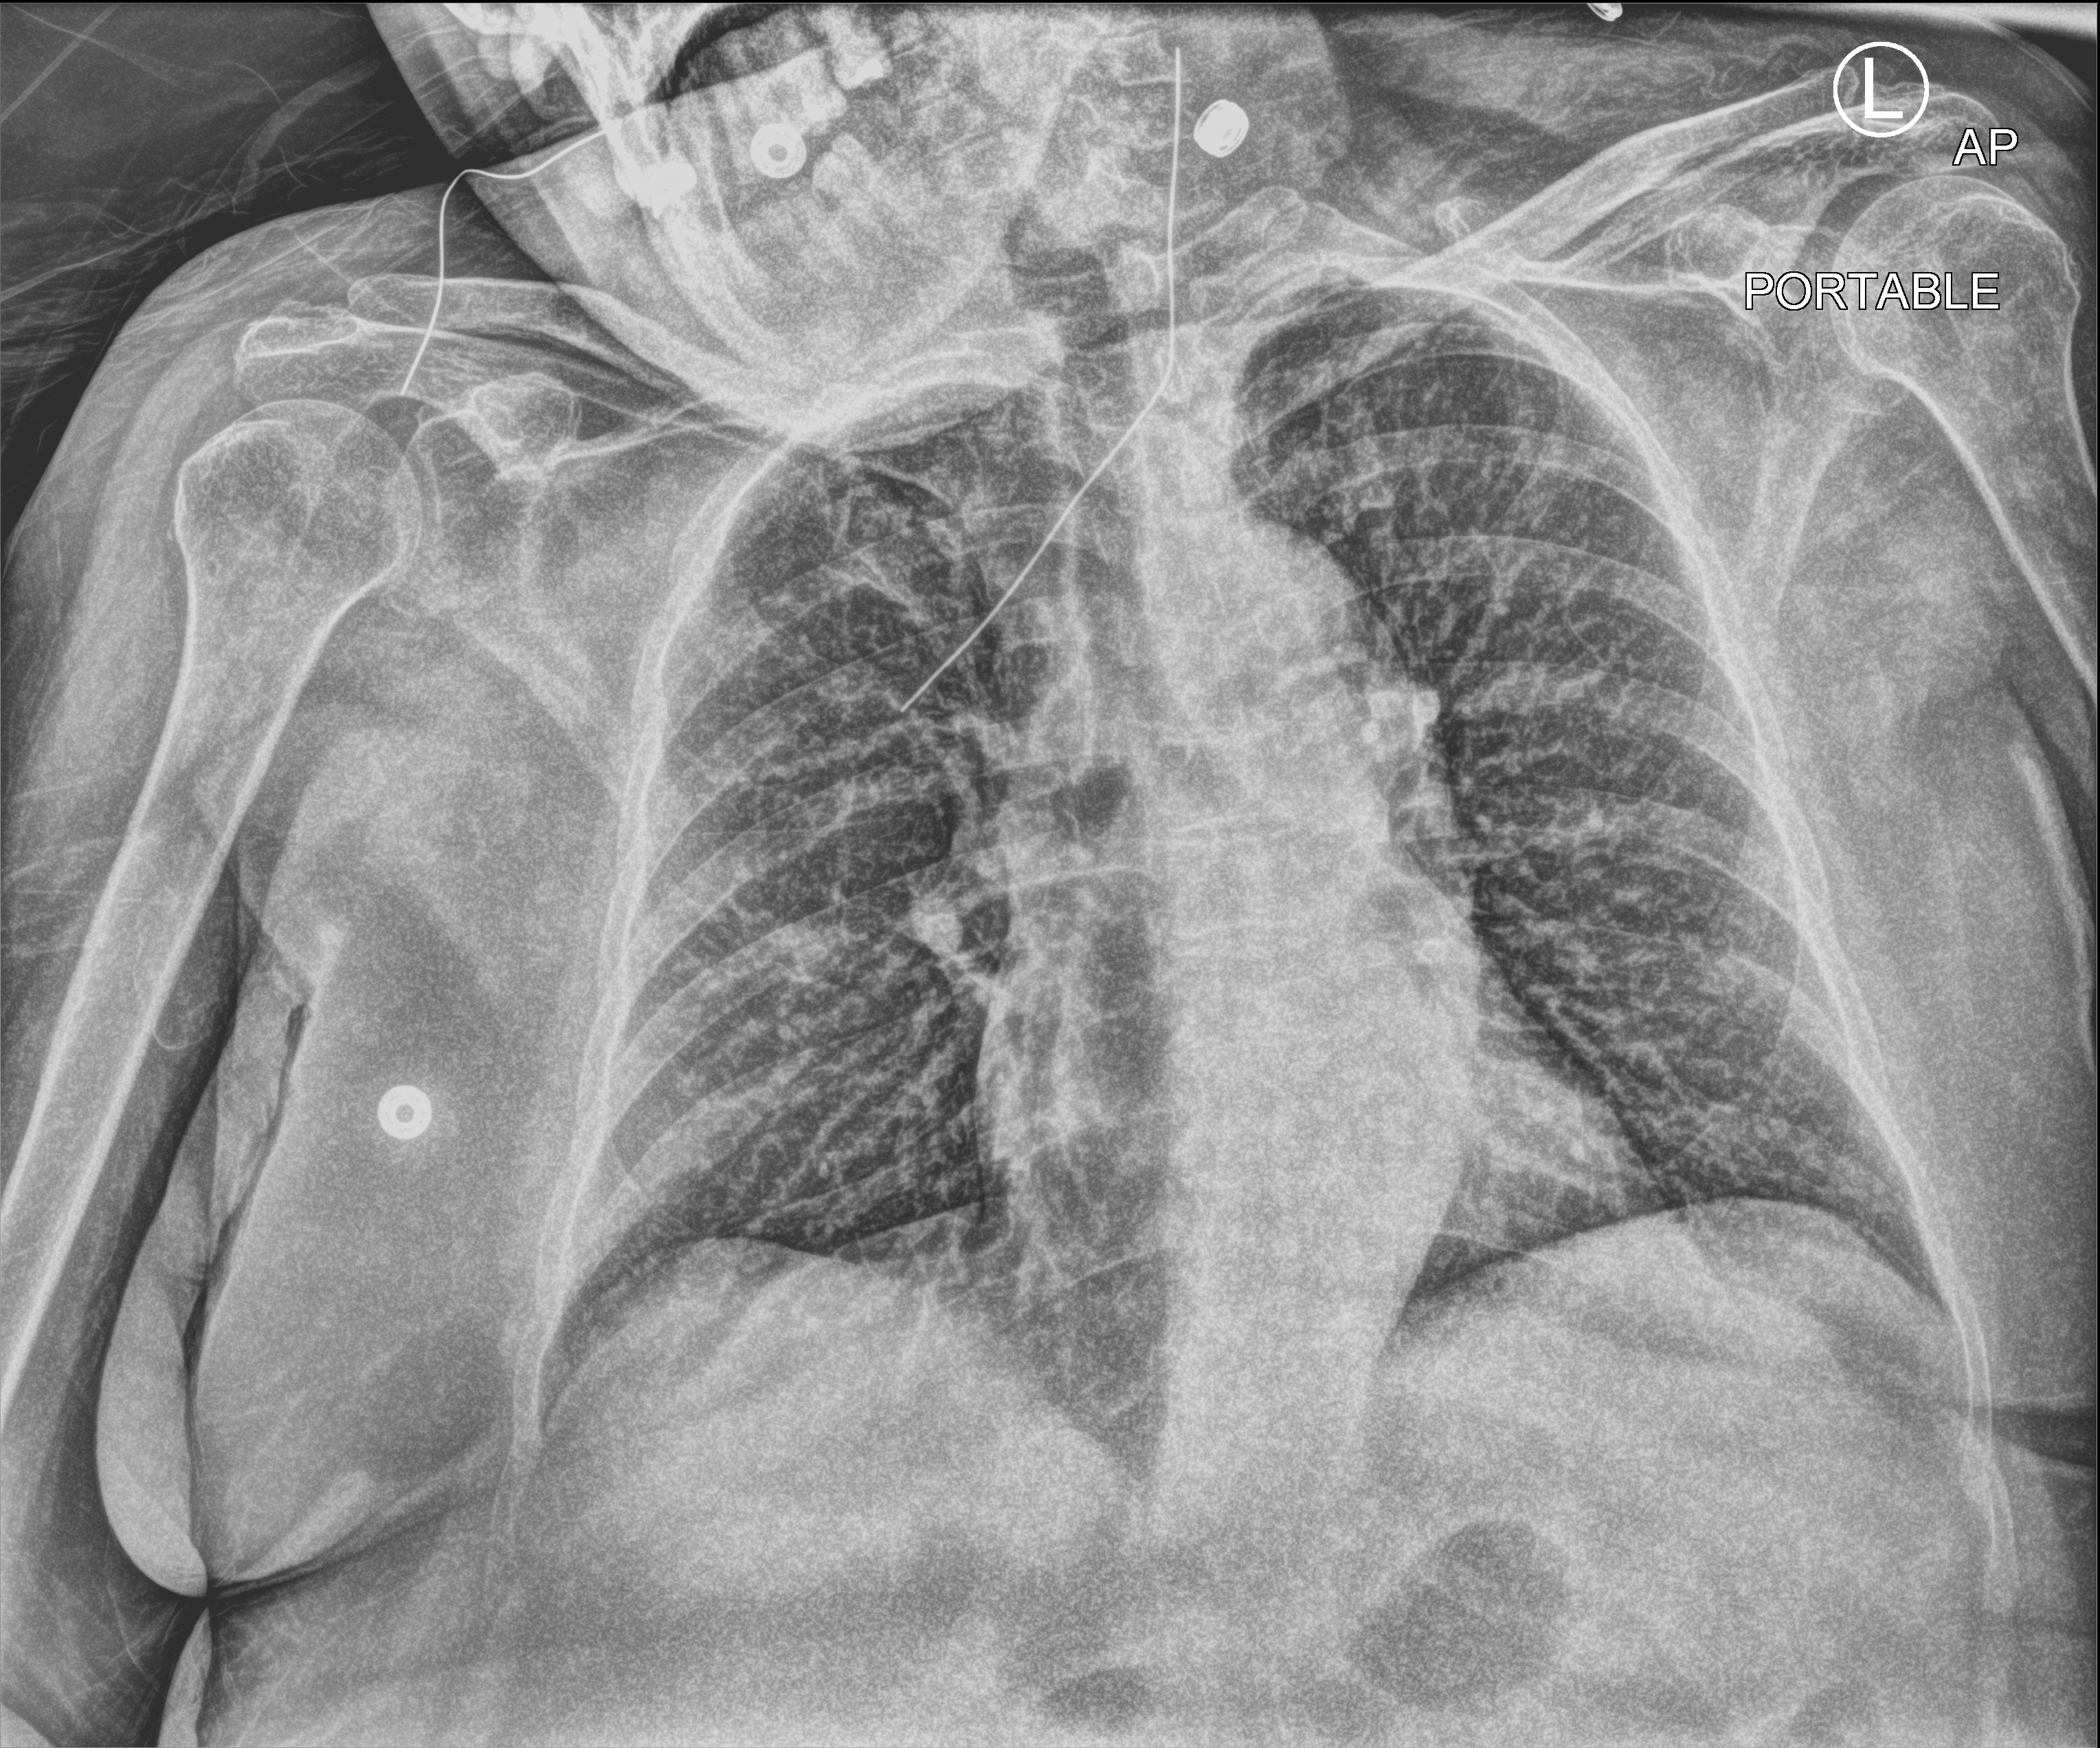
Bedside chest radiograph (computed radiography), anteroposterior (AP) projection. Patient hospitalised with COVID-19; female, aged 18–59 years.
Admission-level facts for this patient (not findings on this image; timing relative to this image not recorded): mechanically ventilated during this hospital stay: no.